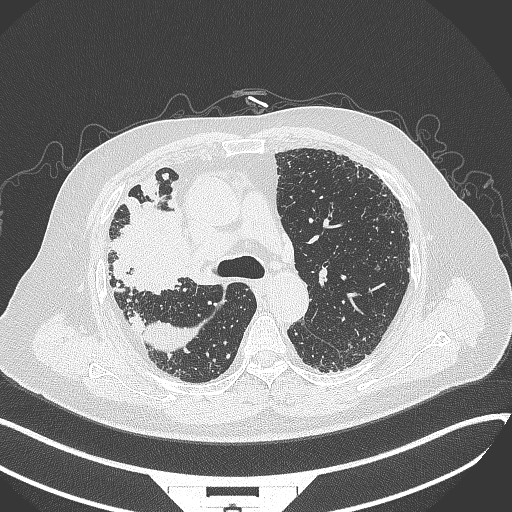
Chest CT, one axial slice. Position 232 of 384 along the scan axis. Lung window (W 1500 / L -600 HU). 1 mm slice thickness. 512 × 512 image matrix, field of view 400 × 400 mm. Patient: male, 69 years. From the clinical record (not read from this slice): clinical TNM (as recorded): T4 N3 M1.
Annotated regions visible in this slice (rectangle marked by the reading radiologist):
- lung tumour (recorded histology: adenocarcinoma): box from (x=111, y=186) to (x=197, y=294) px